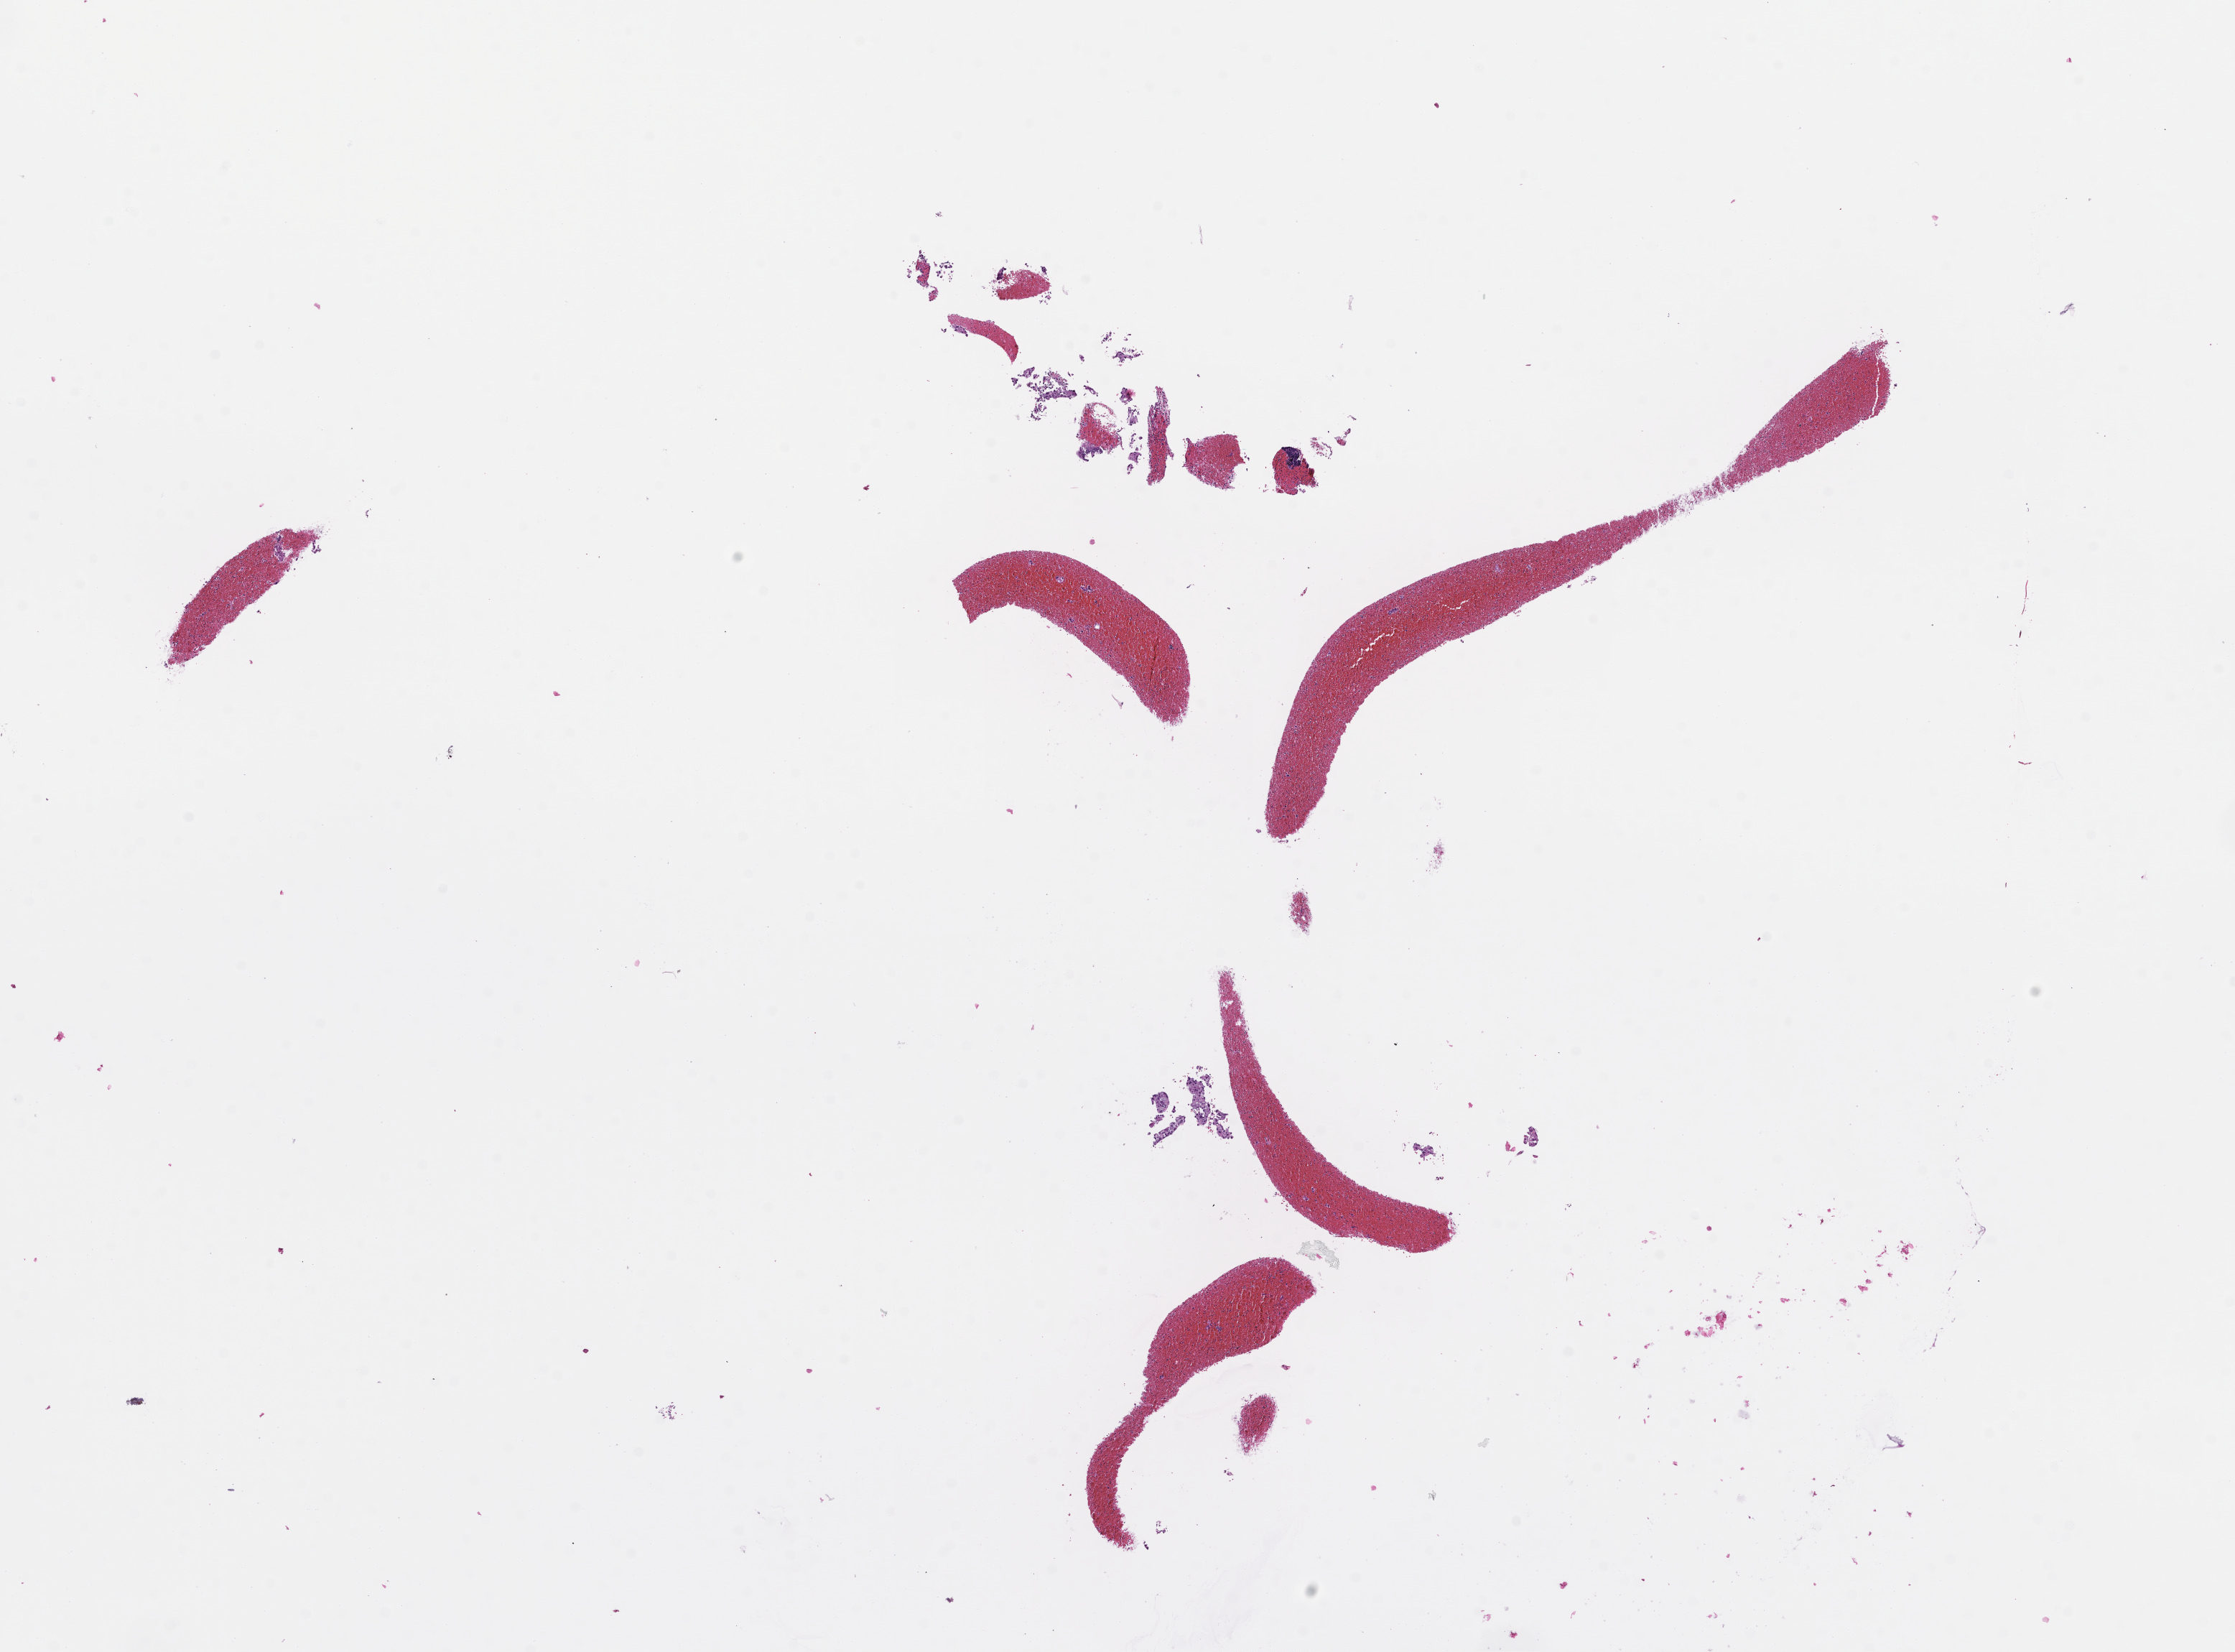
Hematoxylin and eosin (H&E) whole-slide image — whole scanned area (about 12.6 x 9.3 mm) shown as a low-resolution overview; FFPE section; tissue site: lung. Patient: female.
This section: primary tumour tissue. Diagnosis: Non-Small Cell Lung Carcinoma.